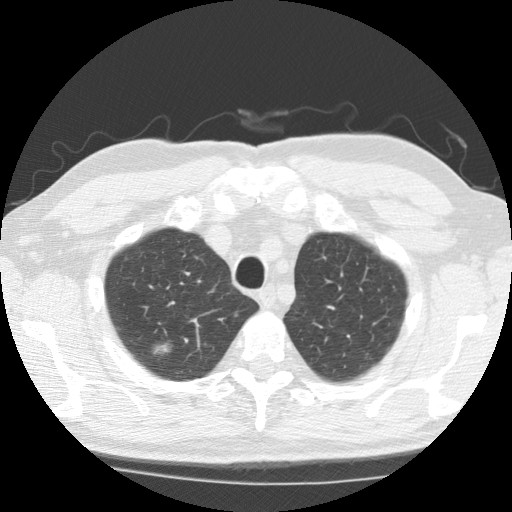
Low-dose screening chest CT, one axial slice. Position 160 of 196 along the scan axis. Reconstruction kernel STANDARD. Lung window (W 1500 / L -600 HU). 2.5 mm slice thickness. 512 × 512 image matrix, field of view 350 × 350 mm.
Structures marked on this image (outlined manually by an expert reader):
- lesion 1 (tumor, upper lobe of right lung): bounding box (x1, y1, x2, y2) in pixels: (153, 342, 171, 357)